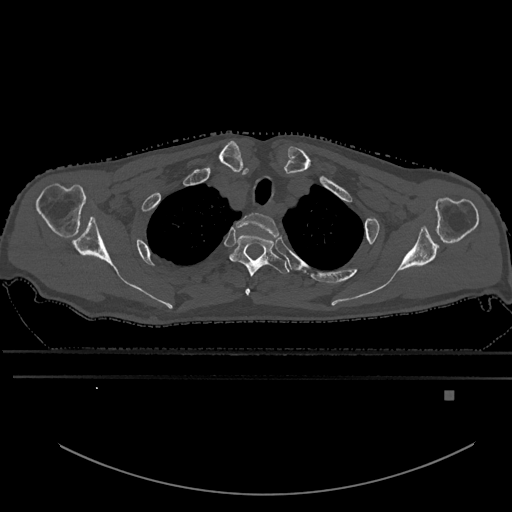
CT including the spine, one axial slice. Slice 502 of 969 in the series (ordered by position). Bone window (W 1800 / L 400 HU). 0.5 mm slice thickness. 512 × 512 image matrix, field of view 456 × 456 mm. Patient: male, 82 years. Case-level facts recorded for this patient, not image findings: primary cancer: prostate; vertebrae with lytic lesions (as recorded): T11, T9, T8, T2.
Structures marked on this image (semi-automatic segmentation, software-assisted and operator-edited):
- T1 vertebra: bounding box <236,212,279,290> (left, top, right, bottom; pixels)
- T2 vertebra: <230,234,289,295>